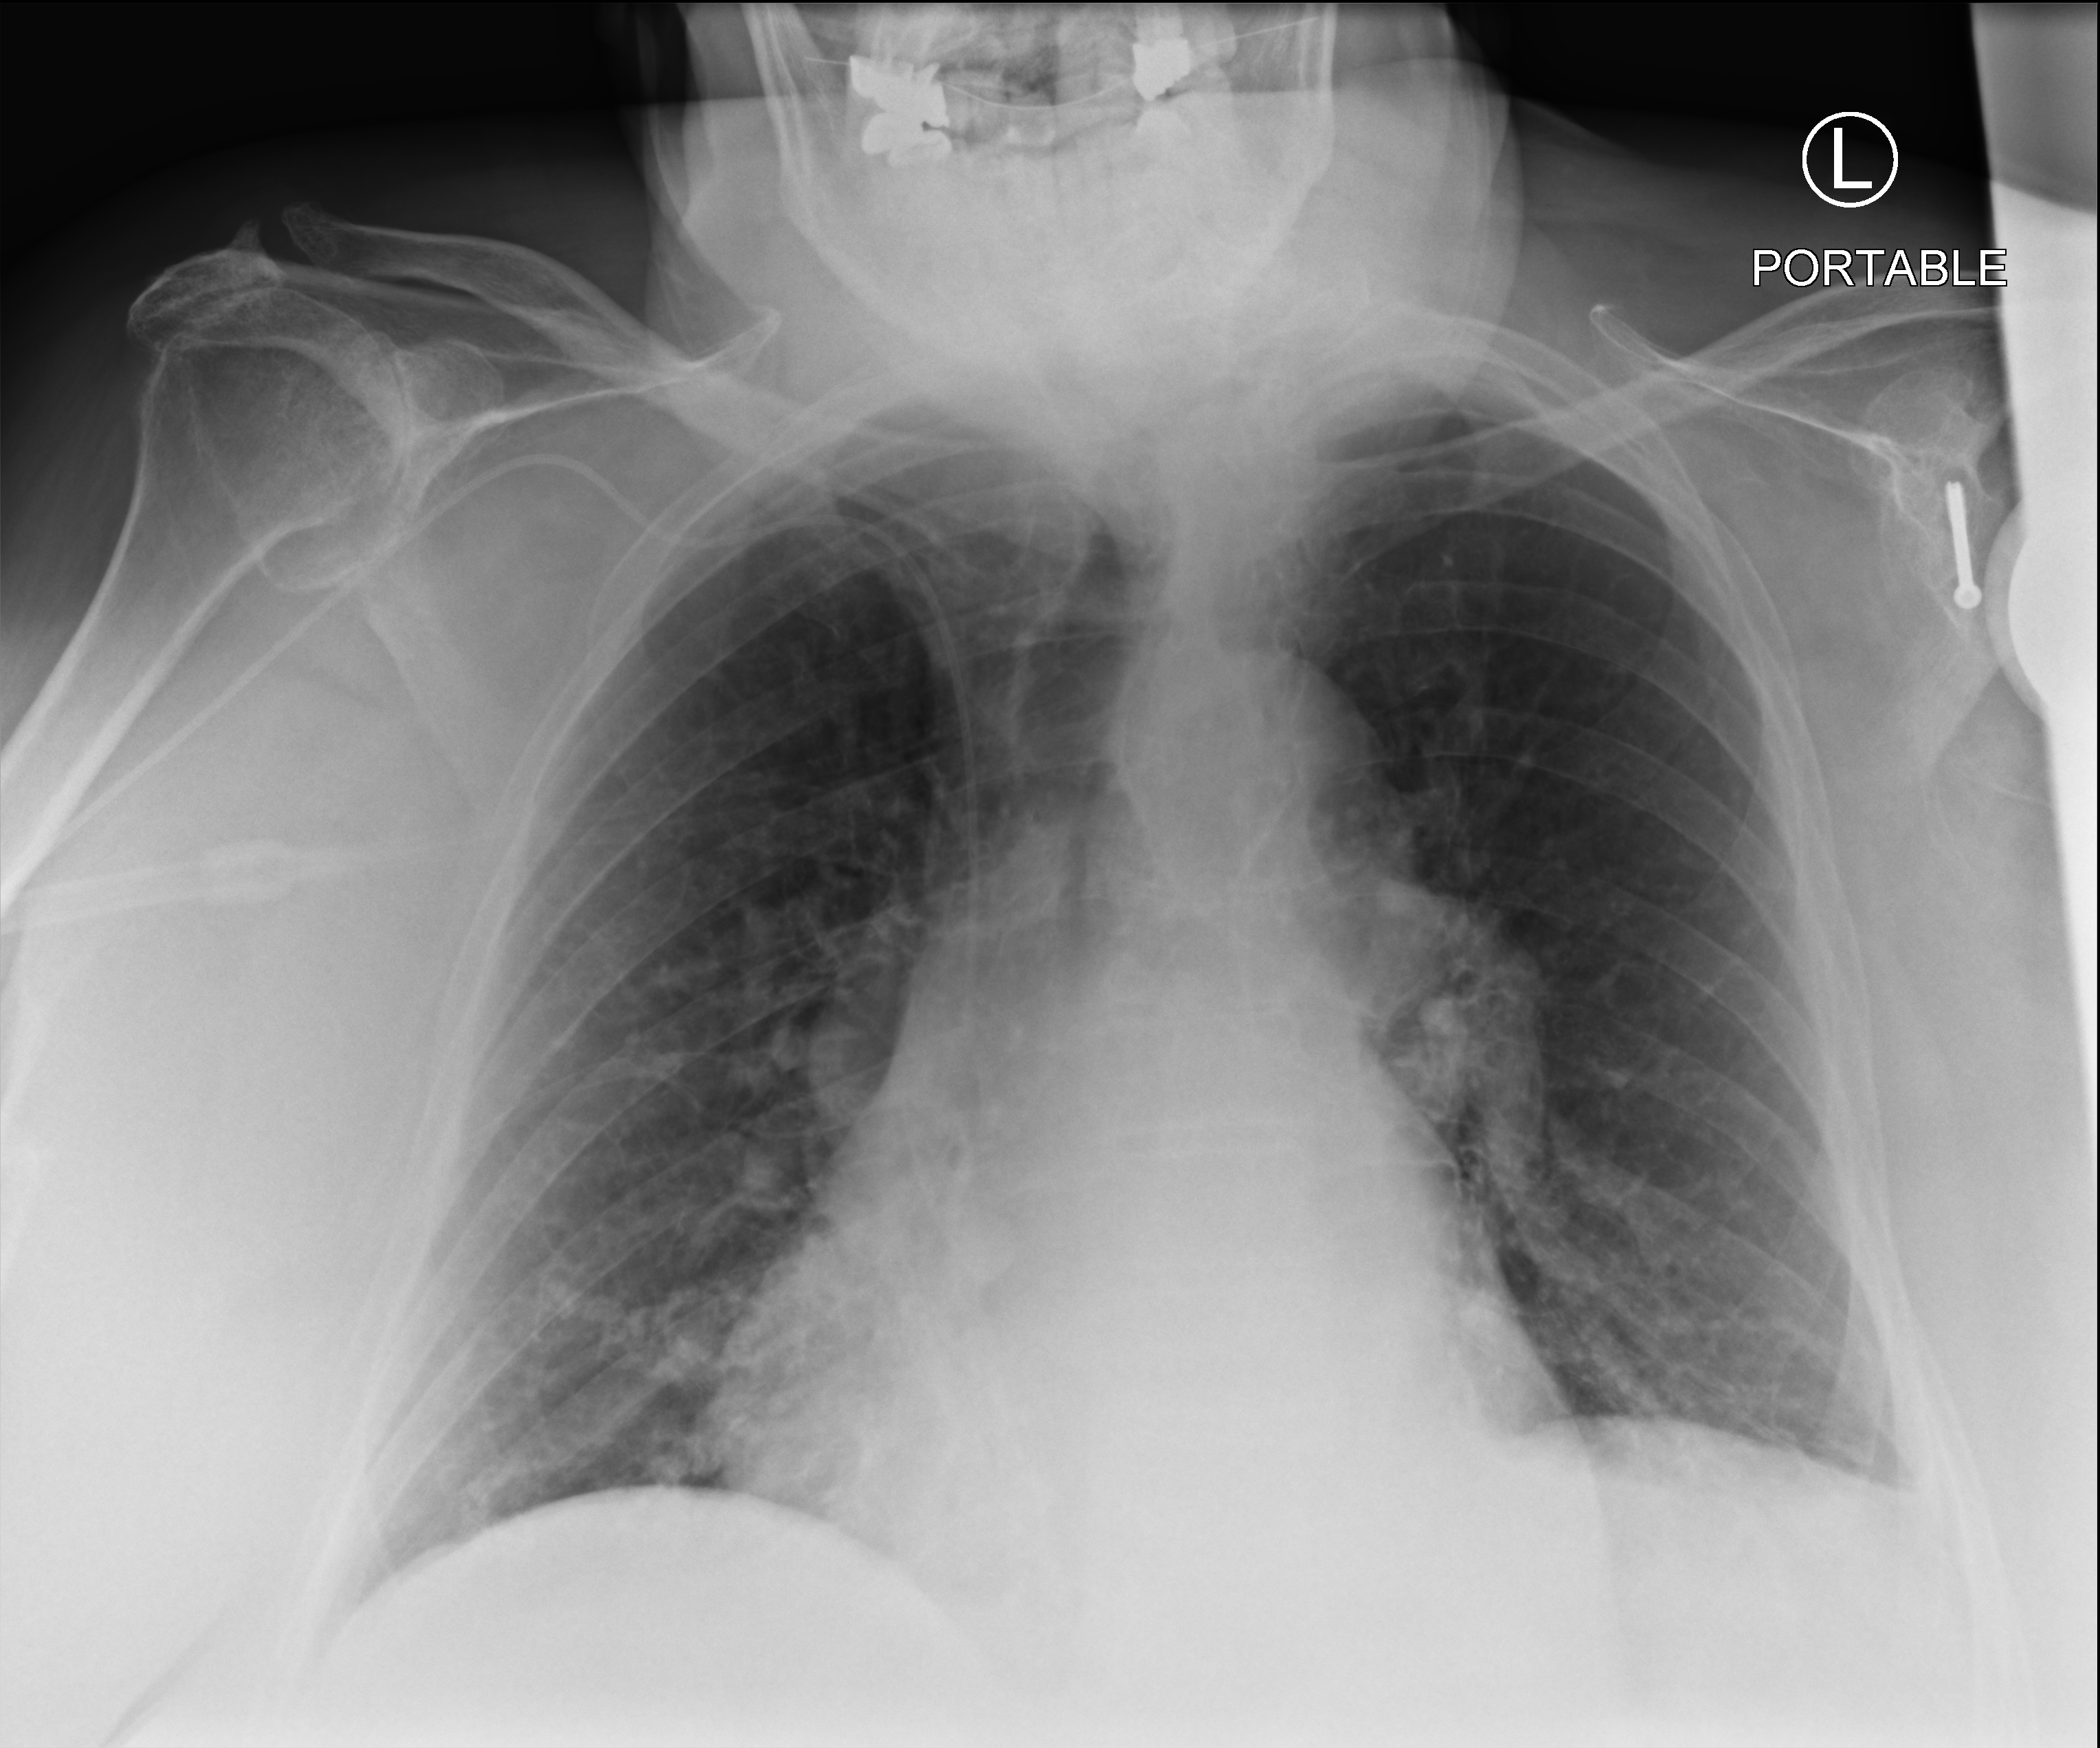
Portable chest radiograph; anteroposterior (AP) projection. Female patient hospitalised with COVID-19, age 75–90 years.
Admission-level facts for this patient (not findings on this image; timing relative to this image not recorded):
- admitted to intensive care during this hospital stay: no